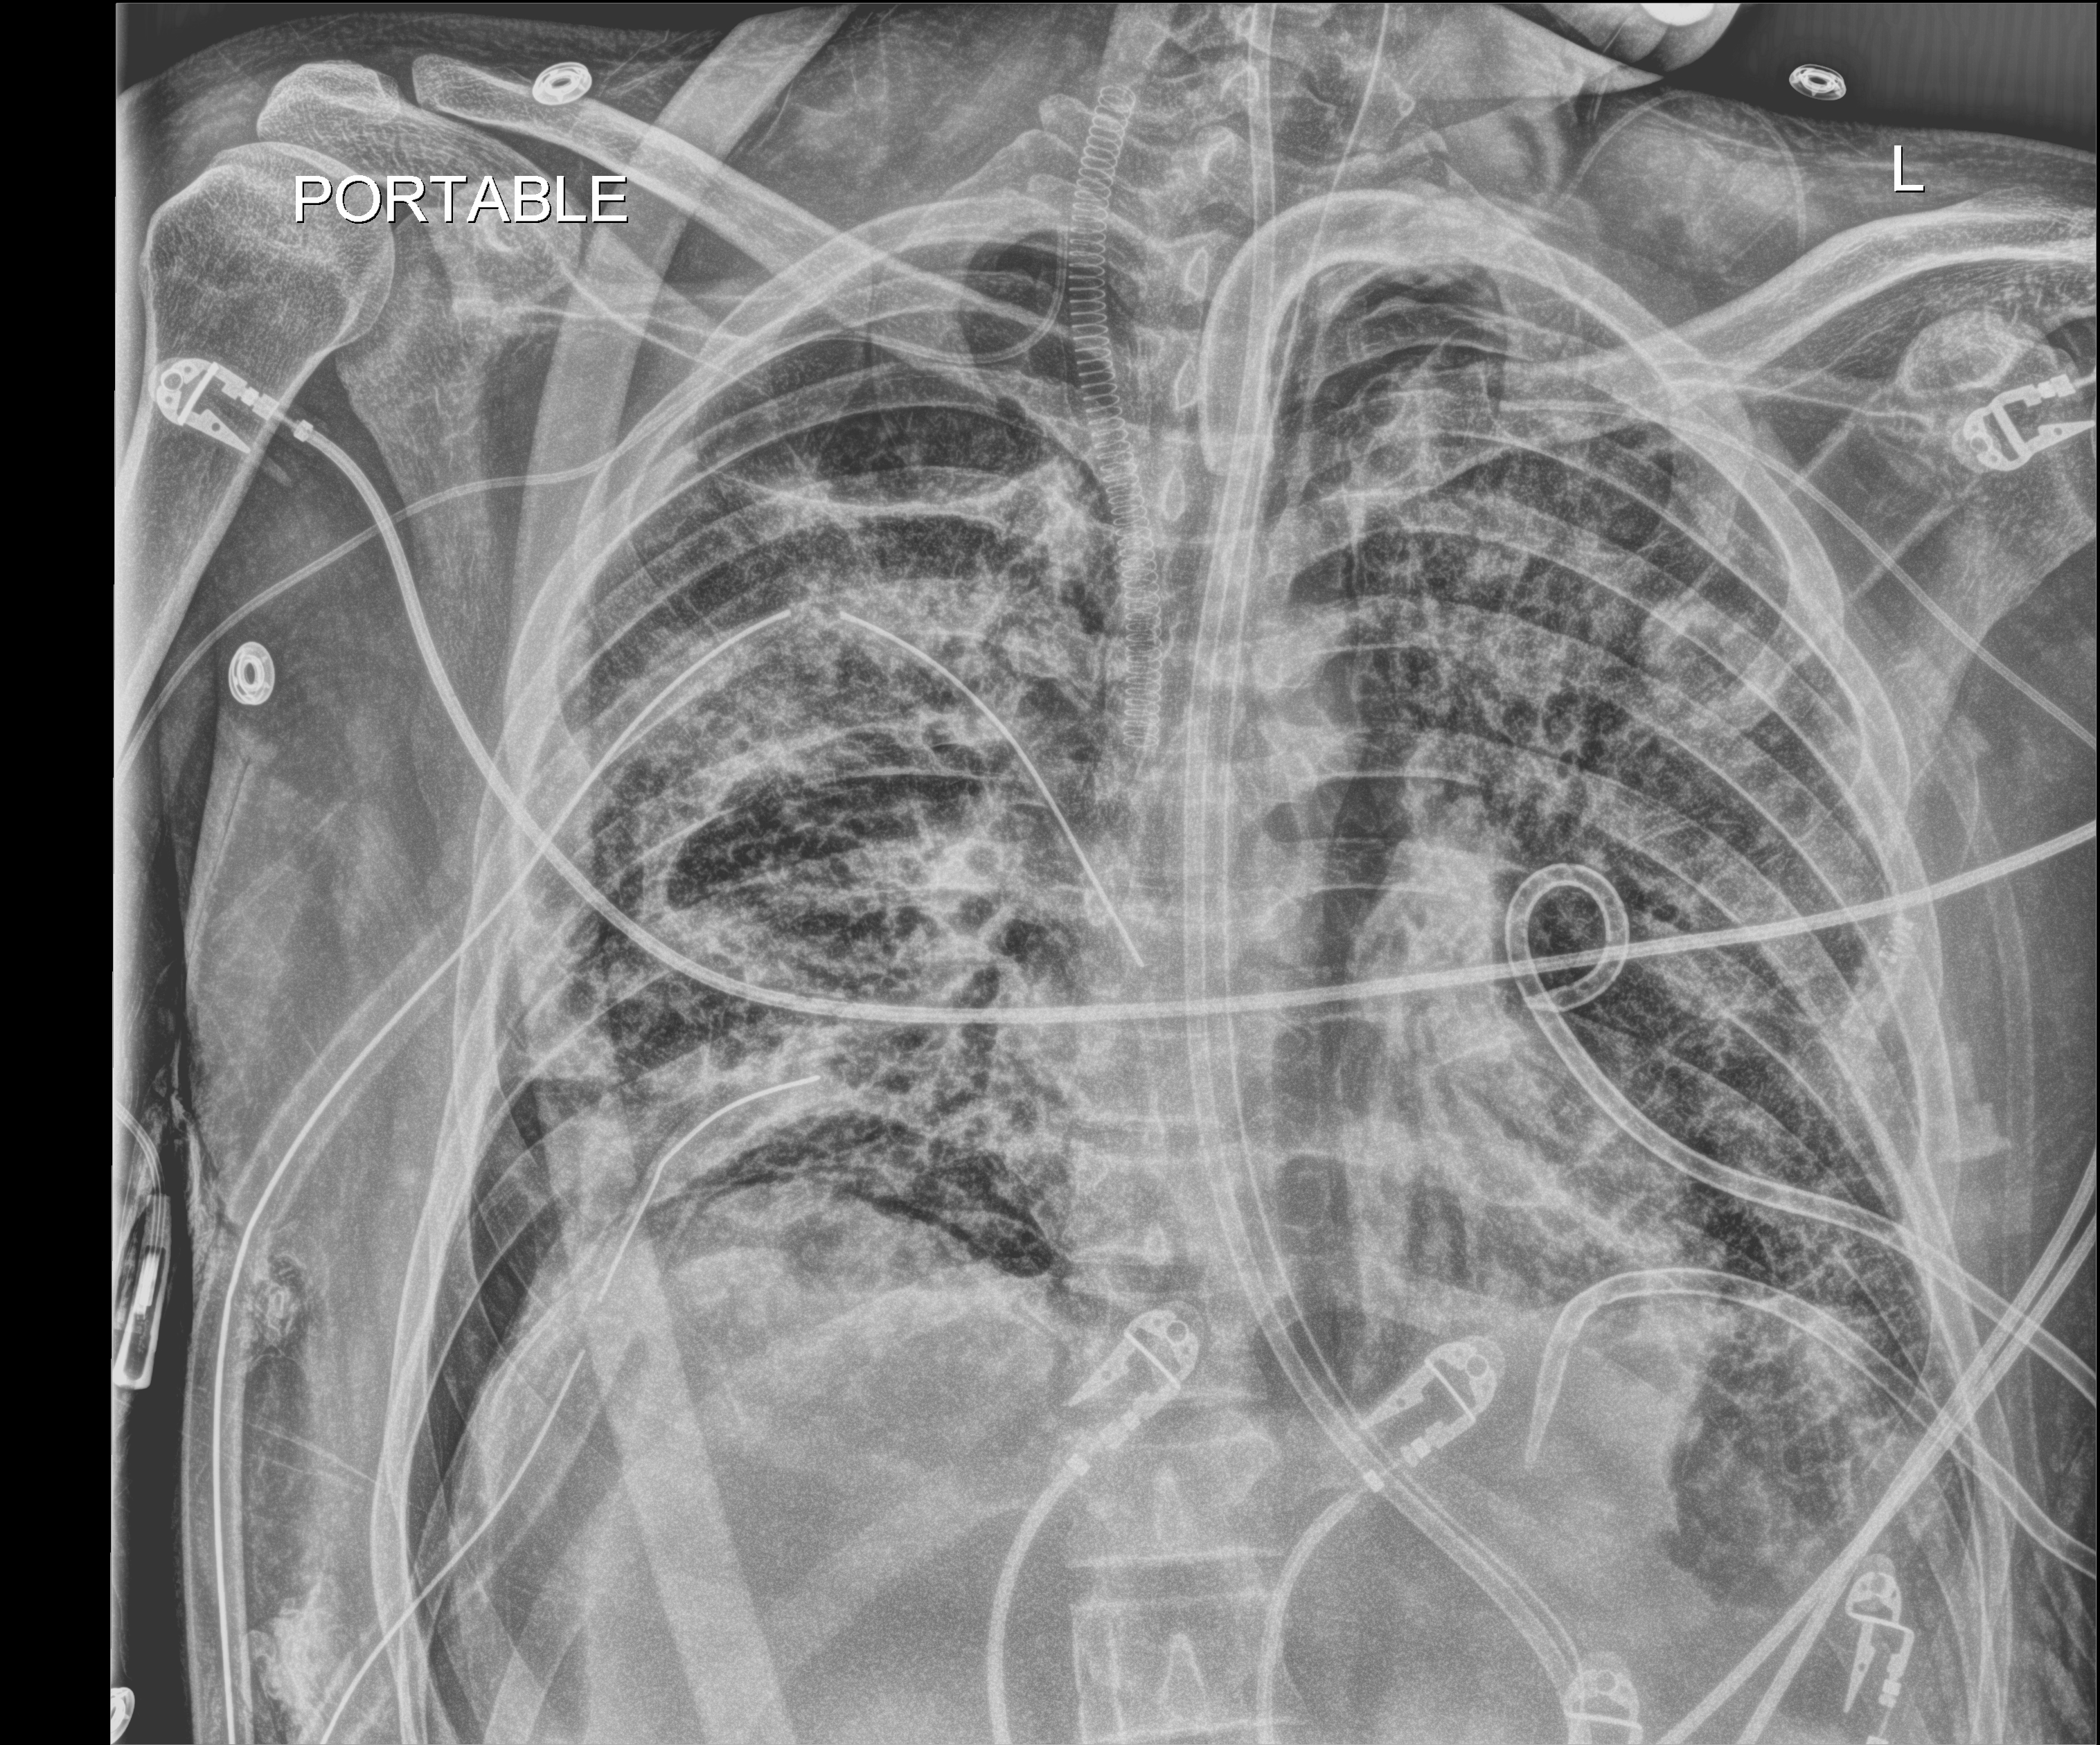
Bedside chest radiograph (digital radiography); anteroposterior (AP) projection. Adult patient hospitalised with COVID-19, age 18–59 years.
Hospital-stay facts (about this admission, not read from this image; timing relative to this image not recorded): mechanically ventilated during this hospital stay: yes.